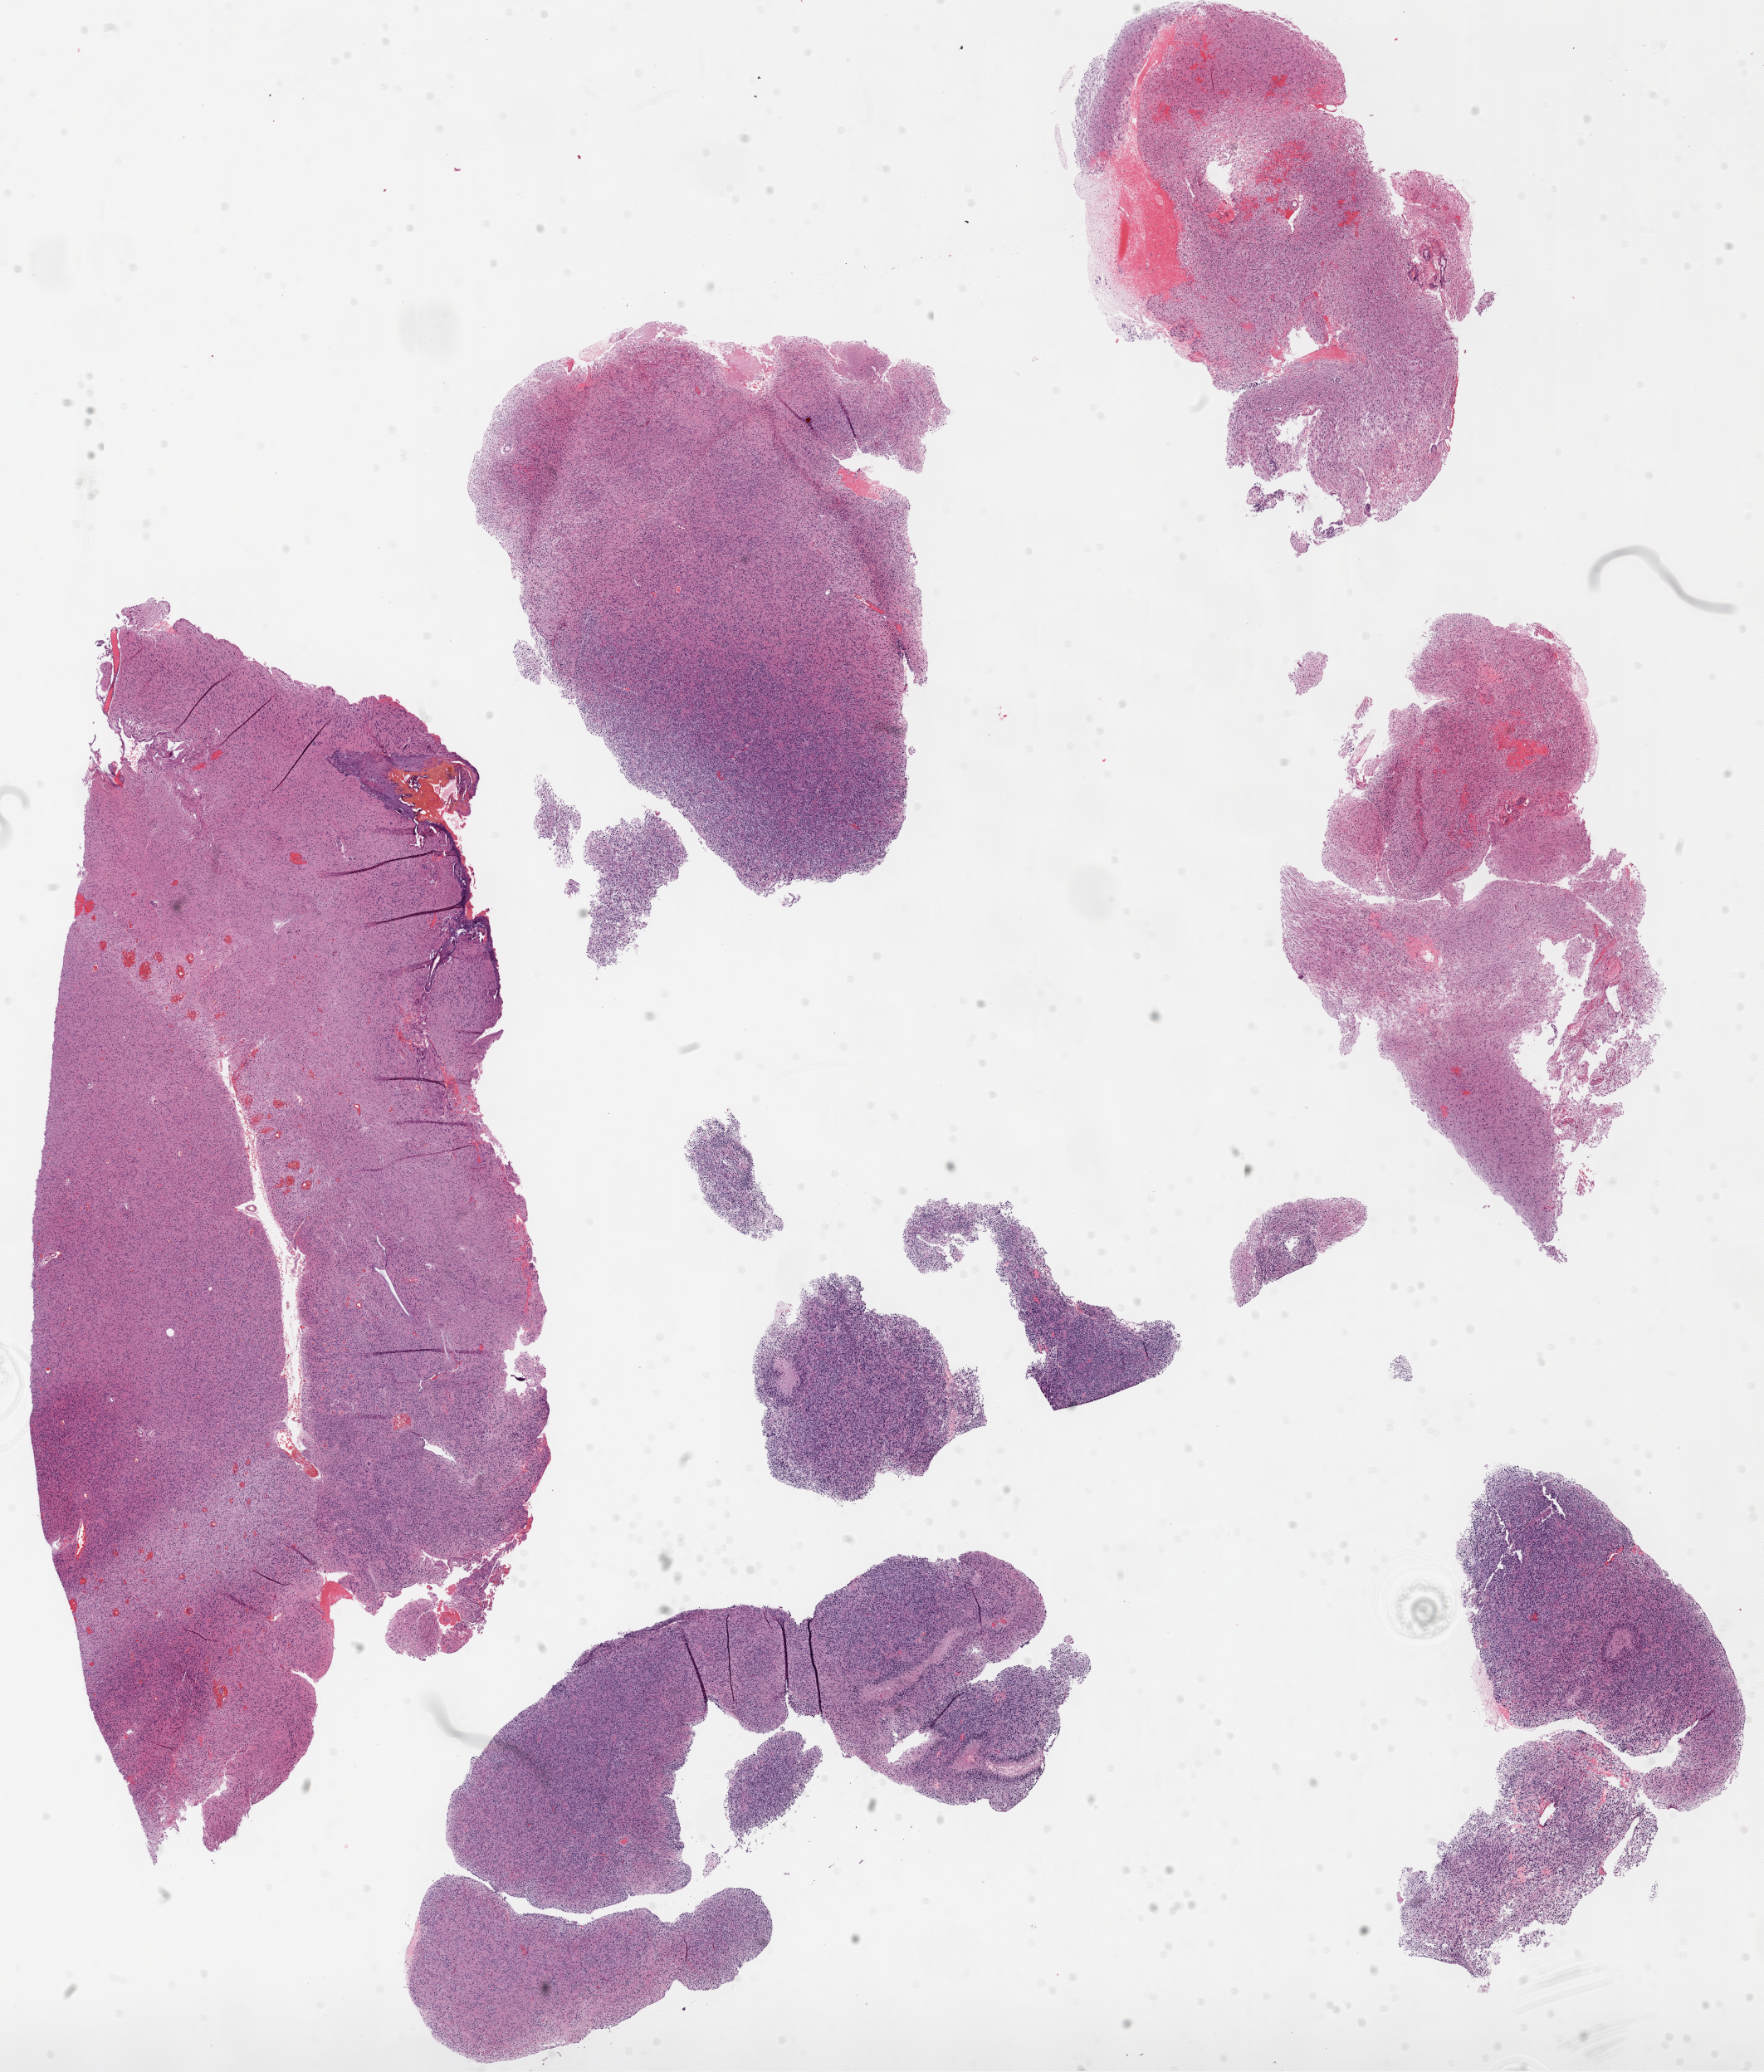
Digitized H&E-stained tissue section (whole slide), shown as a low-resolution overview of the whole scanned area (about 17.1 x 20.0 mm, acquisition: 20x scan), FFPE section, brain, primary tumour sample. Female patient; age at initial diagnosis 63 years.
* pathologic diagnosis: Glioblastoma